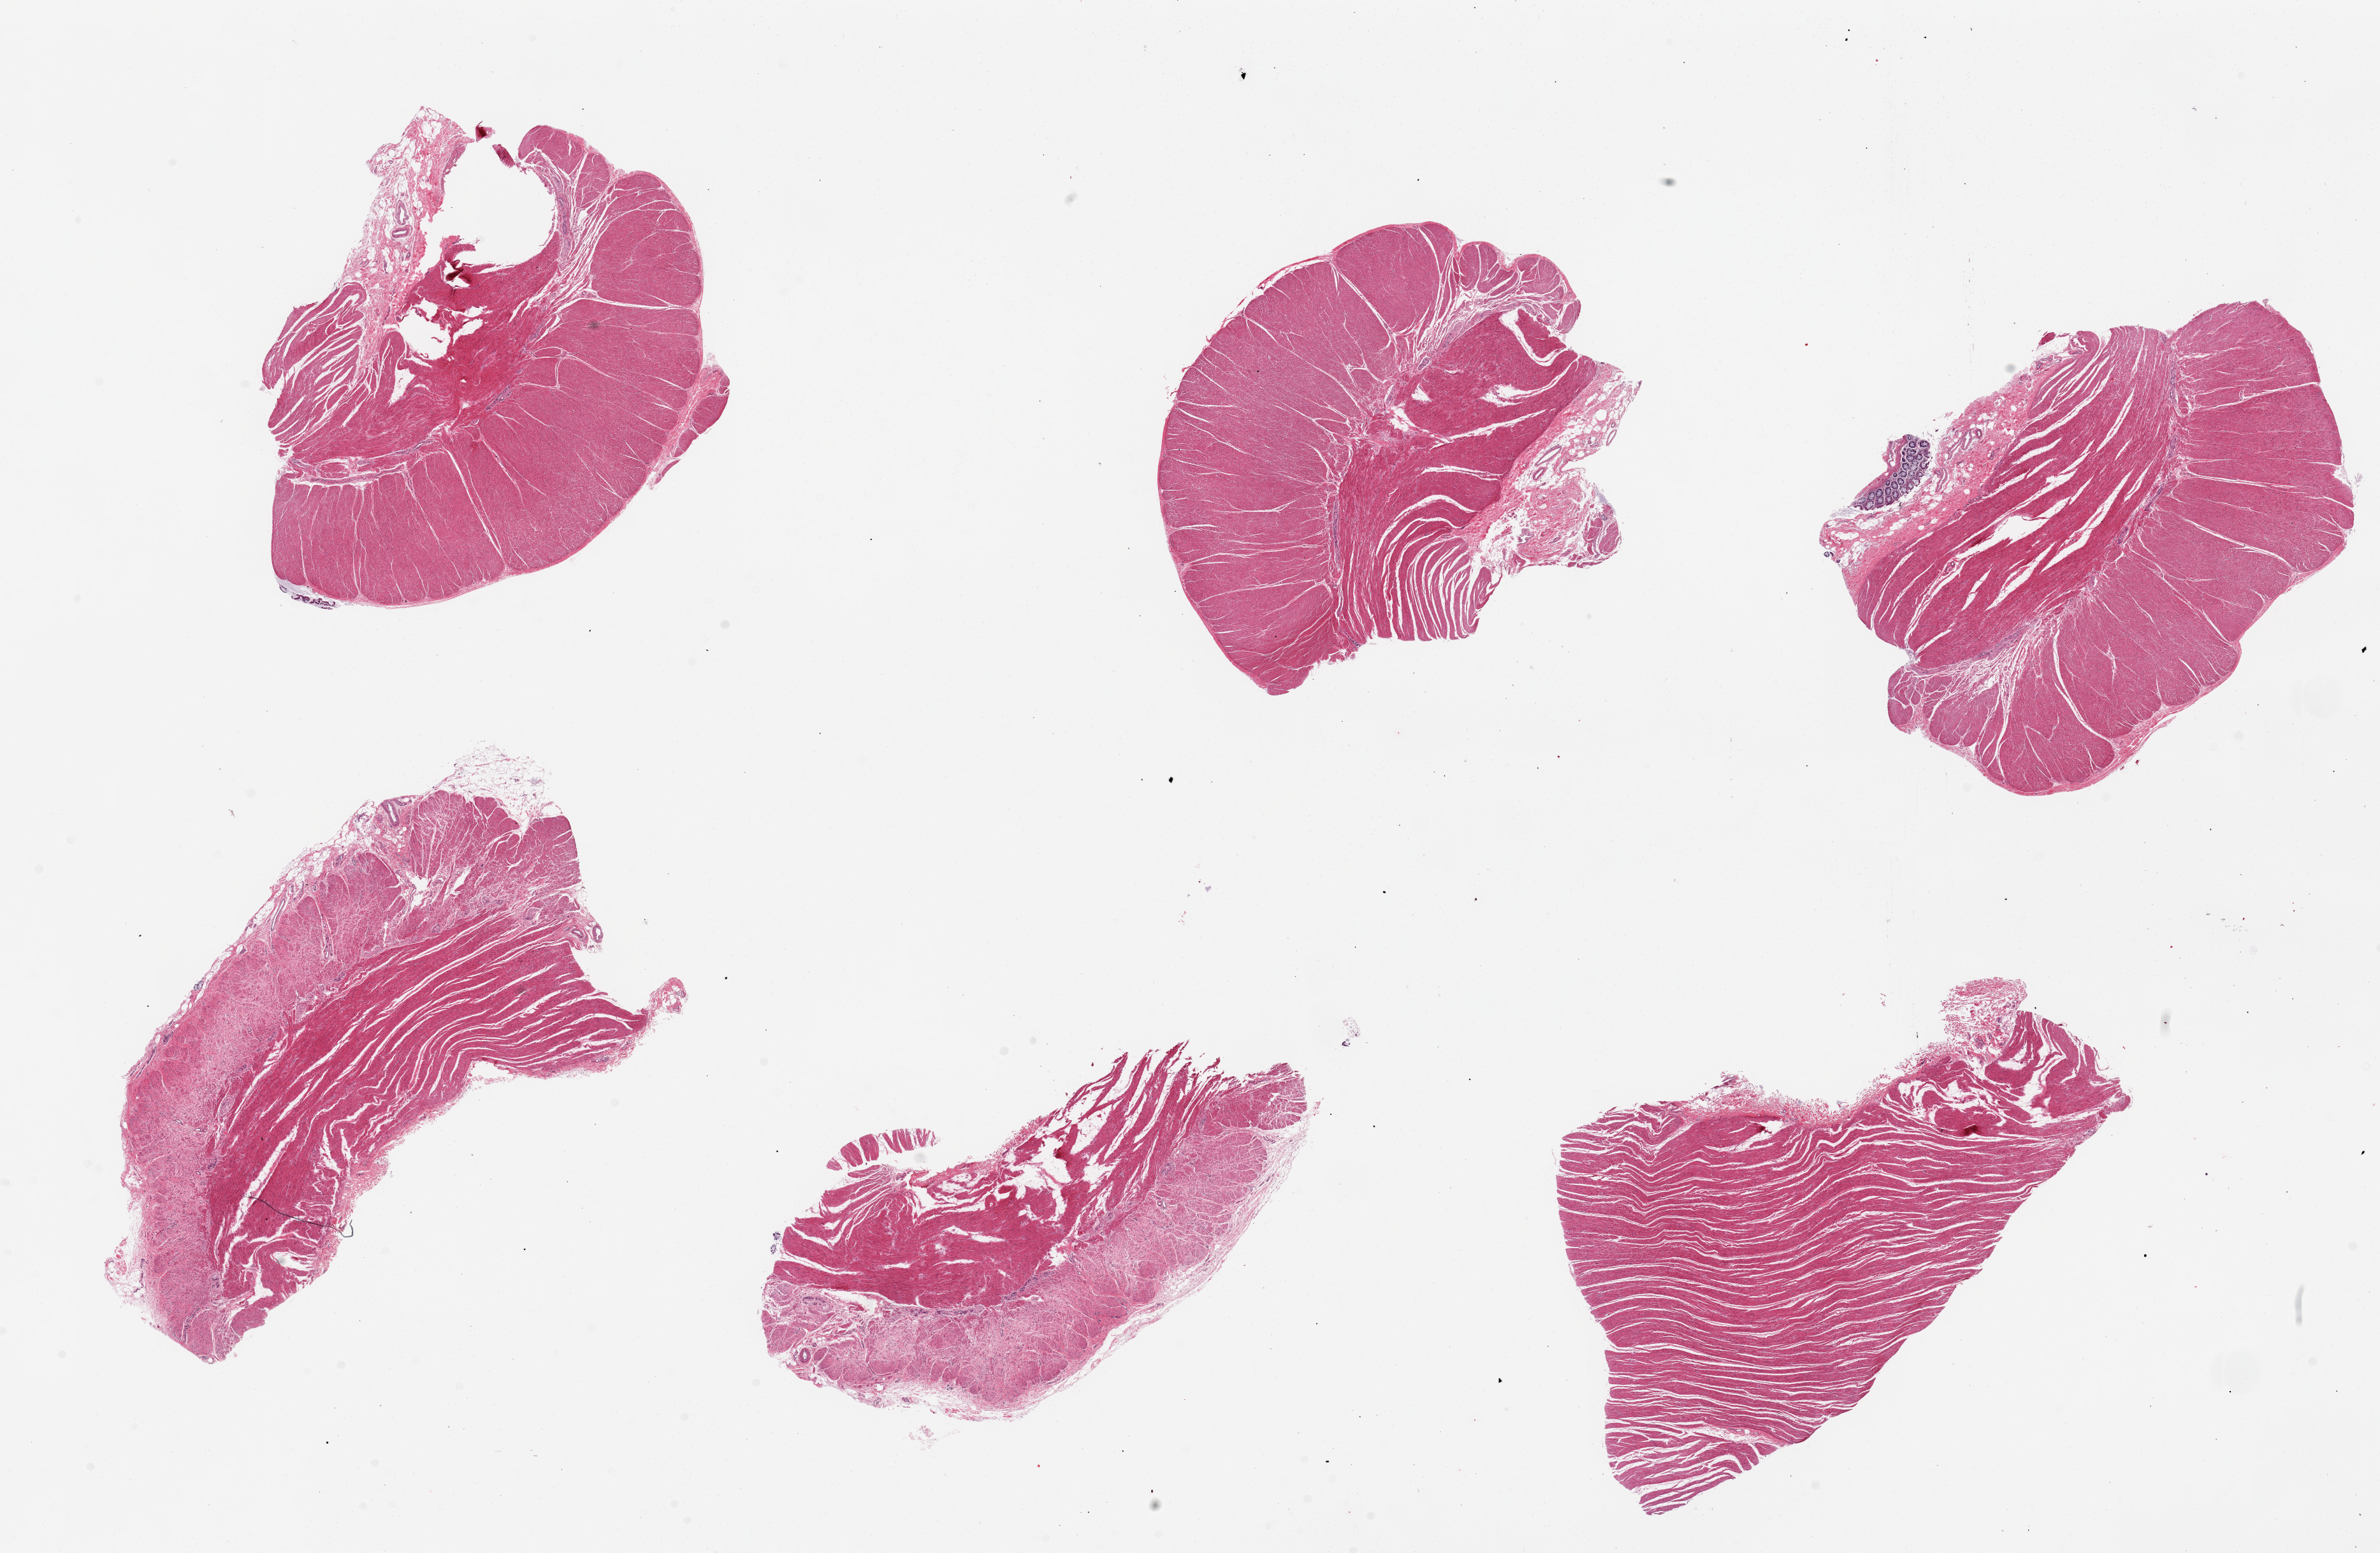
Digitized hematoxylin and eosin (H&E)-stained section, brightfield, low-resolution overview of the scanned area, about 29.5 x 19.3 mm, PAXgene-fixed paraffin-embedded (PFPE) section, target tissue: sigmoid colon, donor tissue sample.
Review note (as recorded): 6 pieces, ranging from 7x4 to 8x5mm; <1% mucosa; mainly muscularis and serosa.